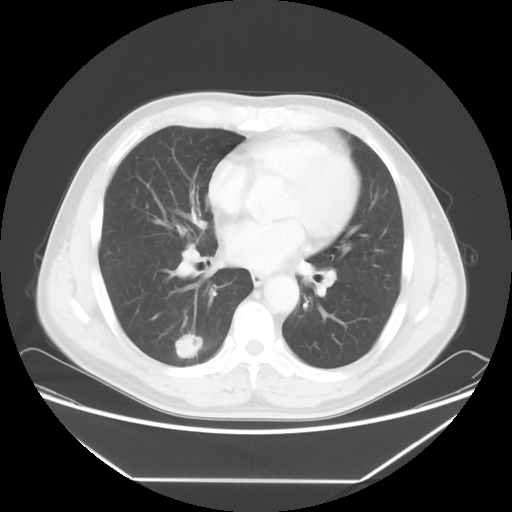
Chest CT, one axial slice. Slice 31 of 65 in the series (ordered by position). Reconstruction kernel STANDARD. 120 kVp. Lung window (W 1500 / L -600 HU). 5 mm slice thickness. 512 × 512 image matrix, field of view 418 × 418 mm. Male patient, age 50 years. From the clinical record (not read from this slice): clinical TNM (as recorded): T1c N0 M0.
Outlined on this slice (rectangle marked by the reading radiologist):
- lung tumour (recorded histology: adenocarcinoma): bounding box (x1, y1, x2, y2) in pixels: (171, 334, 206, 360)